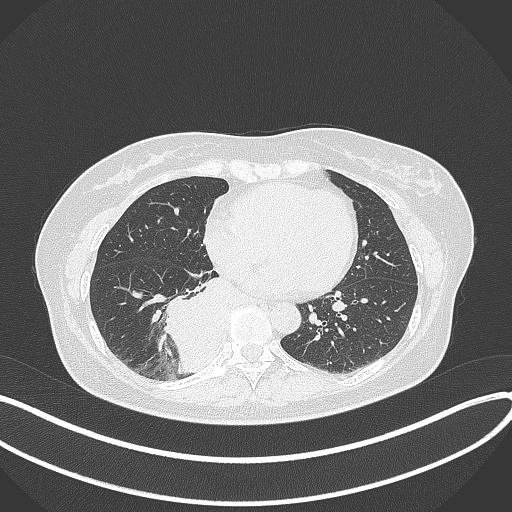
Chest CT, one axial slice. Position 134 of 331 along the scan axis. Reconstruction kernel B70f. 120 kVp. Lung window (W 1500 / L -600 HU). 1 mm slice thickness. 512 × 512 image matrix. Patient: female, 54 years. Case-level facts recorded for this patient, not image findings: clinical TNM (as recorded): T4 N0 M0.
Annotated regions visible in this slice (bounding box drawn by a radiologist):
- lung tumour (recorded histology: adenocarcinoma): box from (x=163, y=271) to (x=241, y=373) px